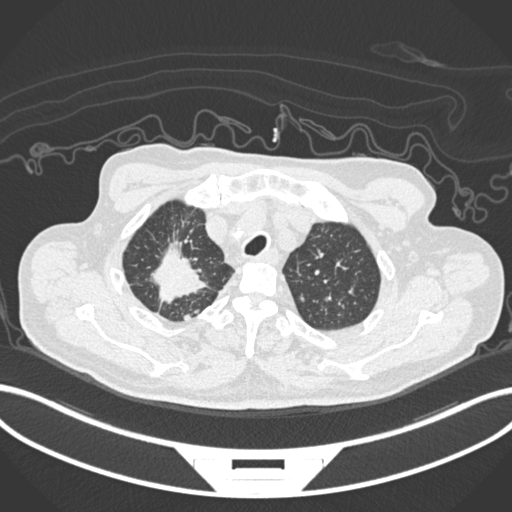
Chest CT, one axial slice. Slice 185 of 207 in the series (ordered by position). Lung window (W 1500 / L -600 HU). 512 × 512 image matrix. Male patient, age 69 years. Case-level facts recorded for this patient, not image findings: clinical TNM (as recorded): T1c N1 M1.
Structures marked on this image (rectangle marked by the reading radiologist):
- lung tumour (recorded histology: adenocarcinoma): bounding box [x1, y1, x2, y2] px = [147, 234, 212, 303]